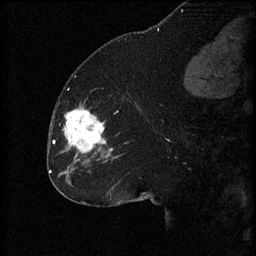
Breast MRI (dynamic contrast-enhanced), one sagittal slice; position 27 of 60 along the scan axis; 3 images stored at this slice position (order not interpretable as contrast timing); 1.5 T; TE 4.2 ms, TR 8.2 ms; 2 mm slice thickness; 256 × 256 image matrix. Female patient, age 32 years.
Annotated regions visible in this slice (semi-automatically segmented with operator editing):
- analysis volume of interest (the breast-tissue region the enhancement analysis was run in; not a lesion): box from (x=60, y=106) to (x=111, y=165) px
- tumour enhancement mask (voxels above the 70 % enhancement threshold inside the analysis volume of interest): (x=62, y=108)–(x=106, y=153)